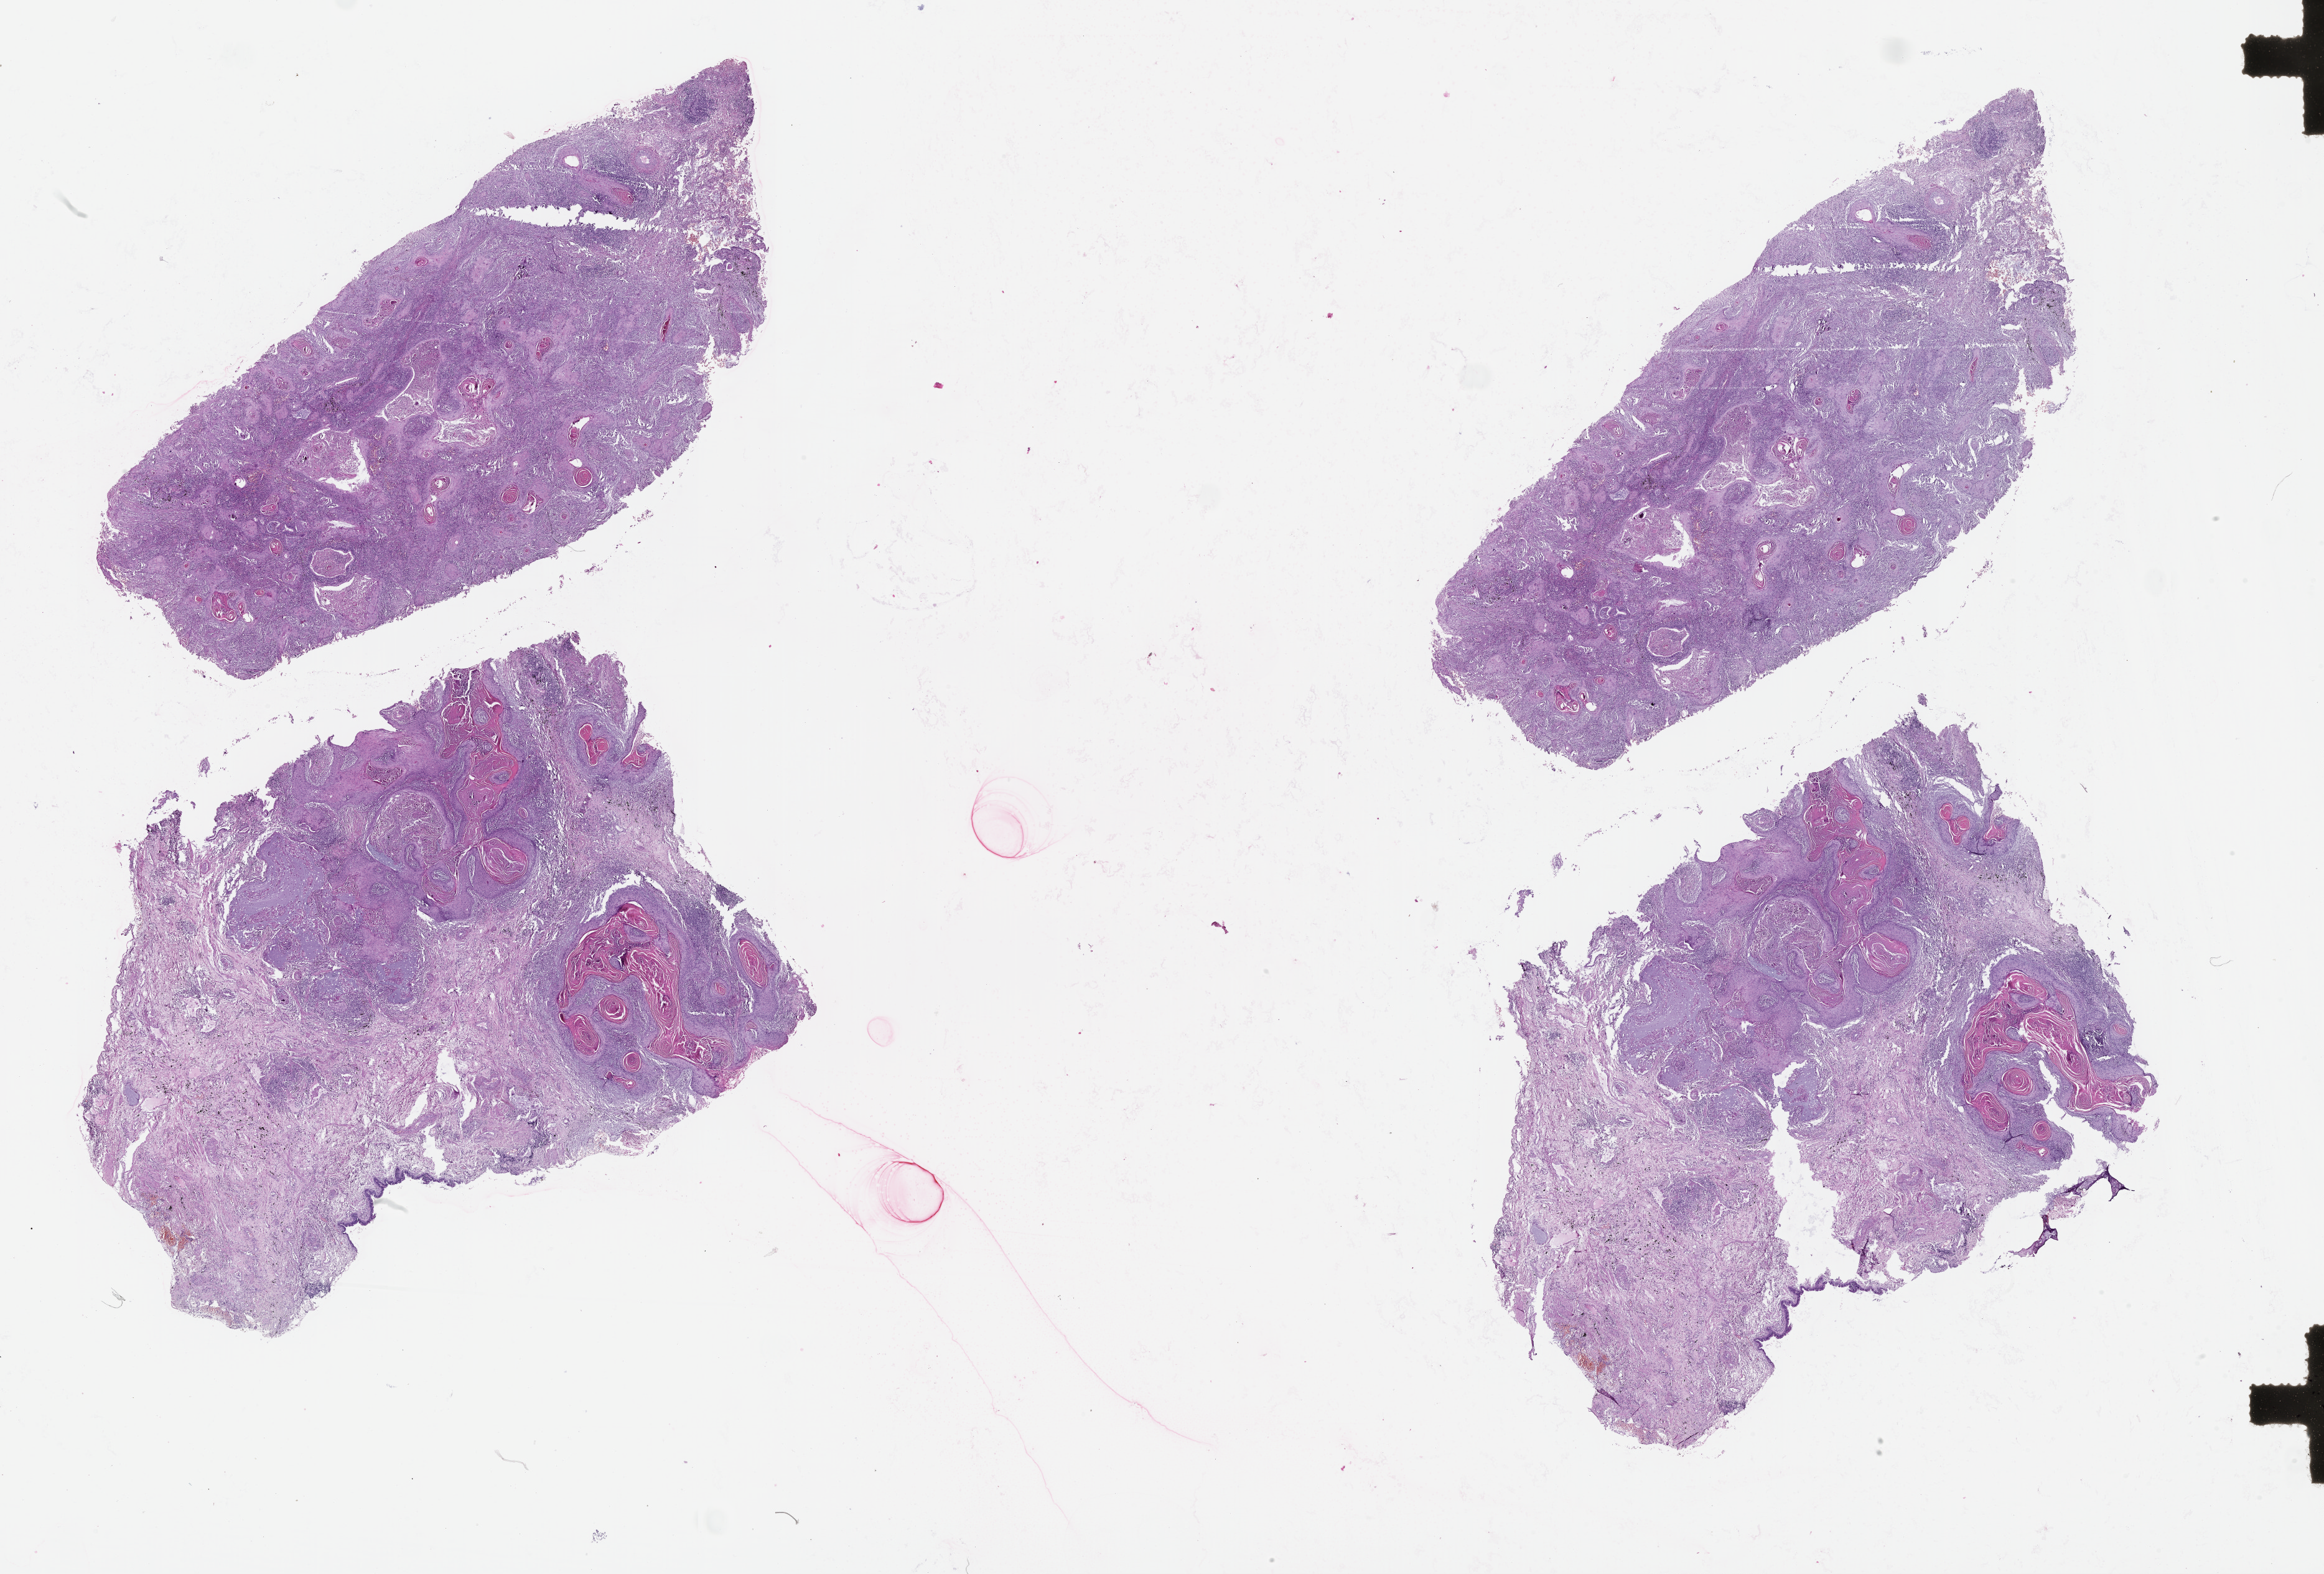
Digitized Hematoxylin and eosin (H&E) stained tissue section (whole slide) — shown as a low-resolution overview of the whole scanned area (about 30.1 x 20.4 mm), tumour tissue sample, lung. Male, 72 y/o.
* patient diagnosis (cohort enrolment): squamous cell carcinoma (lung)